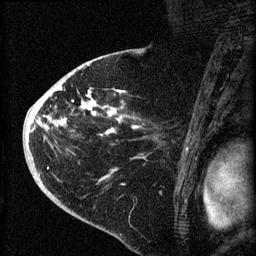
Breast MRI (dynamic contrast-enhanced), one sagittal slice; slice 44 of 60 in the series (ordered by position); dynamic contrast-enhanced series, image 2 of 4 at this slice position (ordered by acquisition); 1.5 T; TE 4.2 ms, TR 8.2 ms; 2 mm slice thickness; 256 × 256 image matrix. Patient: female, 71 years.
Annotated regions visible in this slice (semi-automatic segmentation, software-assisted and operator-edited):
- analysis volume of interest (the breast-tissue region the enhancement analysis was run in; not a lesion): bounding box [x1, y1, x2, y2] px = [35, 75, 150, 190]
- tumour enhancement mask (voxels above the 70 % enhancement threshold inside the analysis volume of interest): [35, 82, 138, 181]